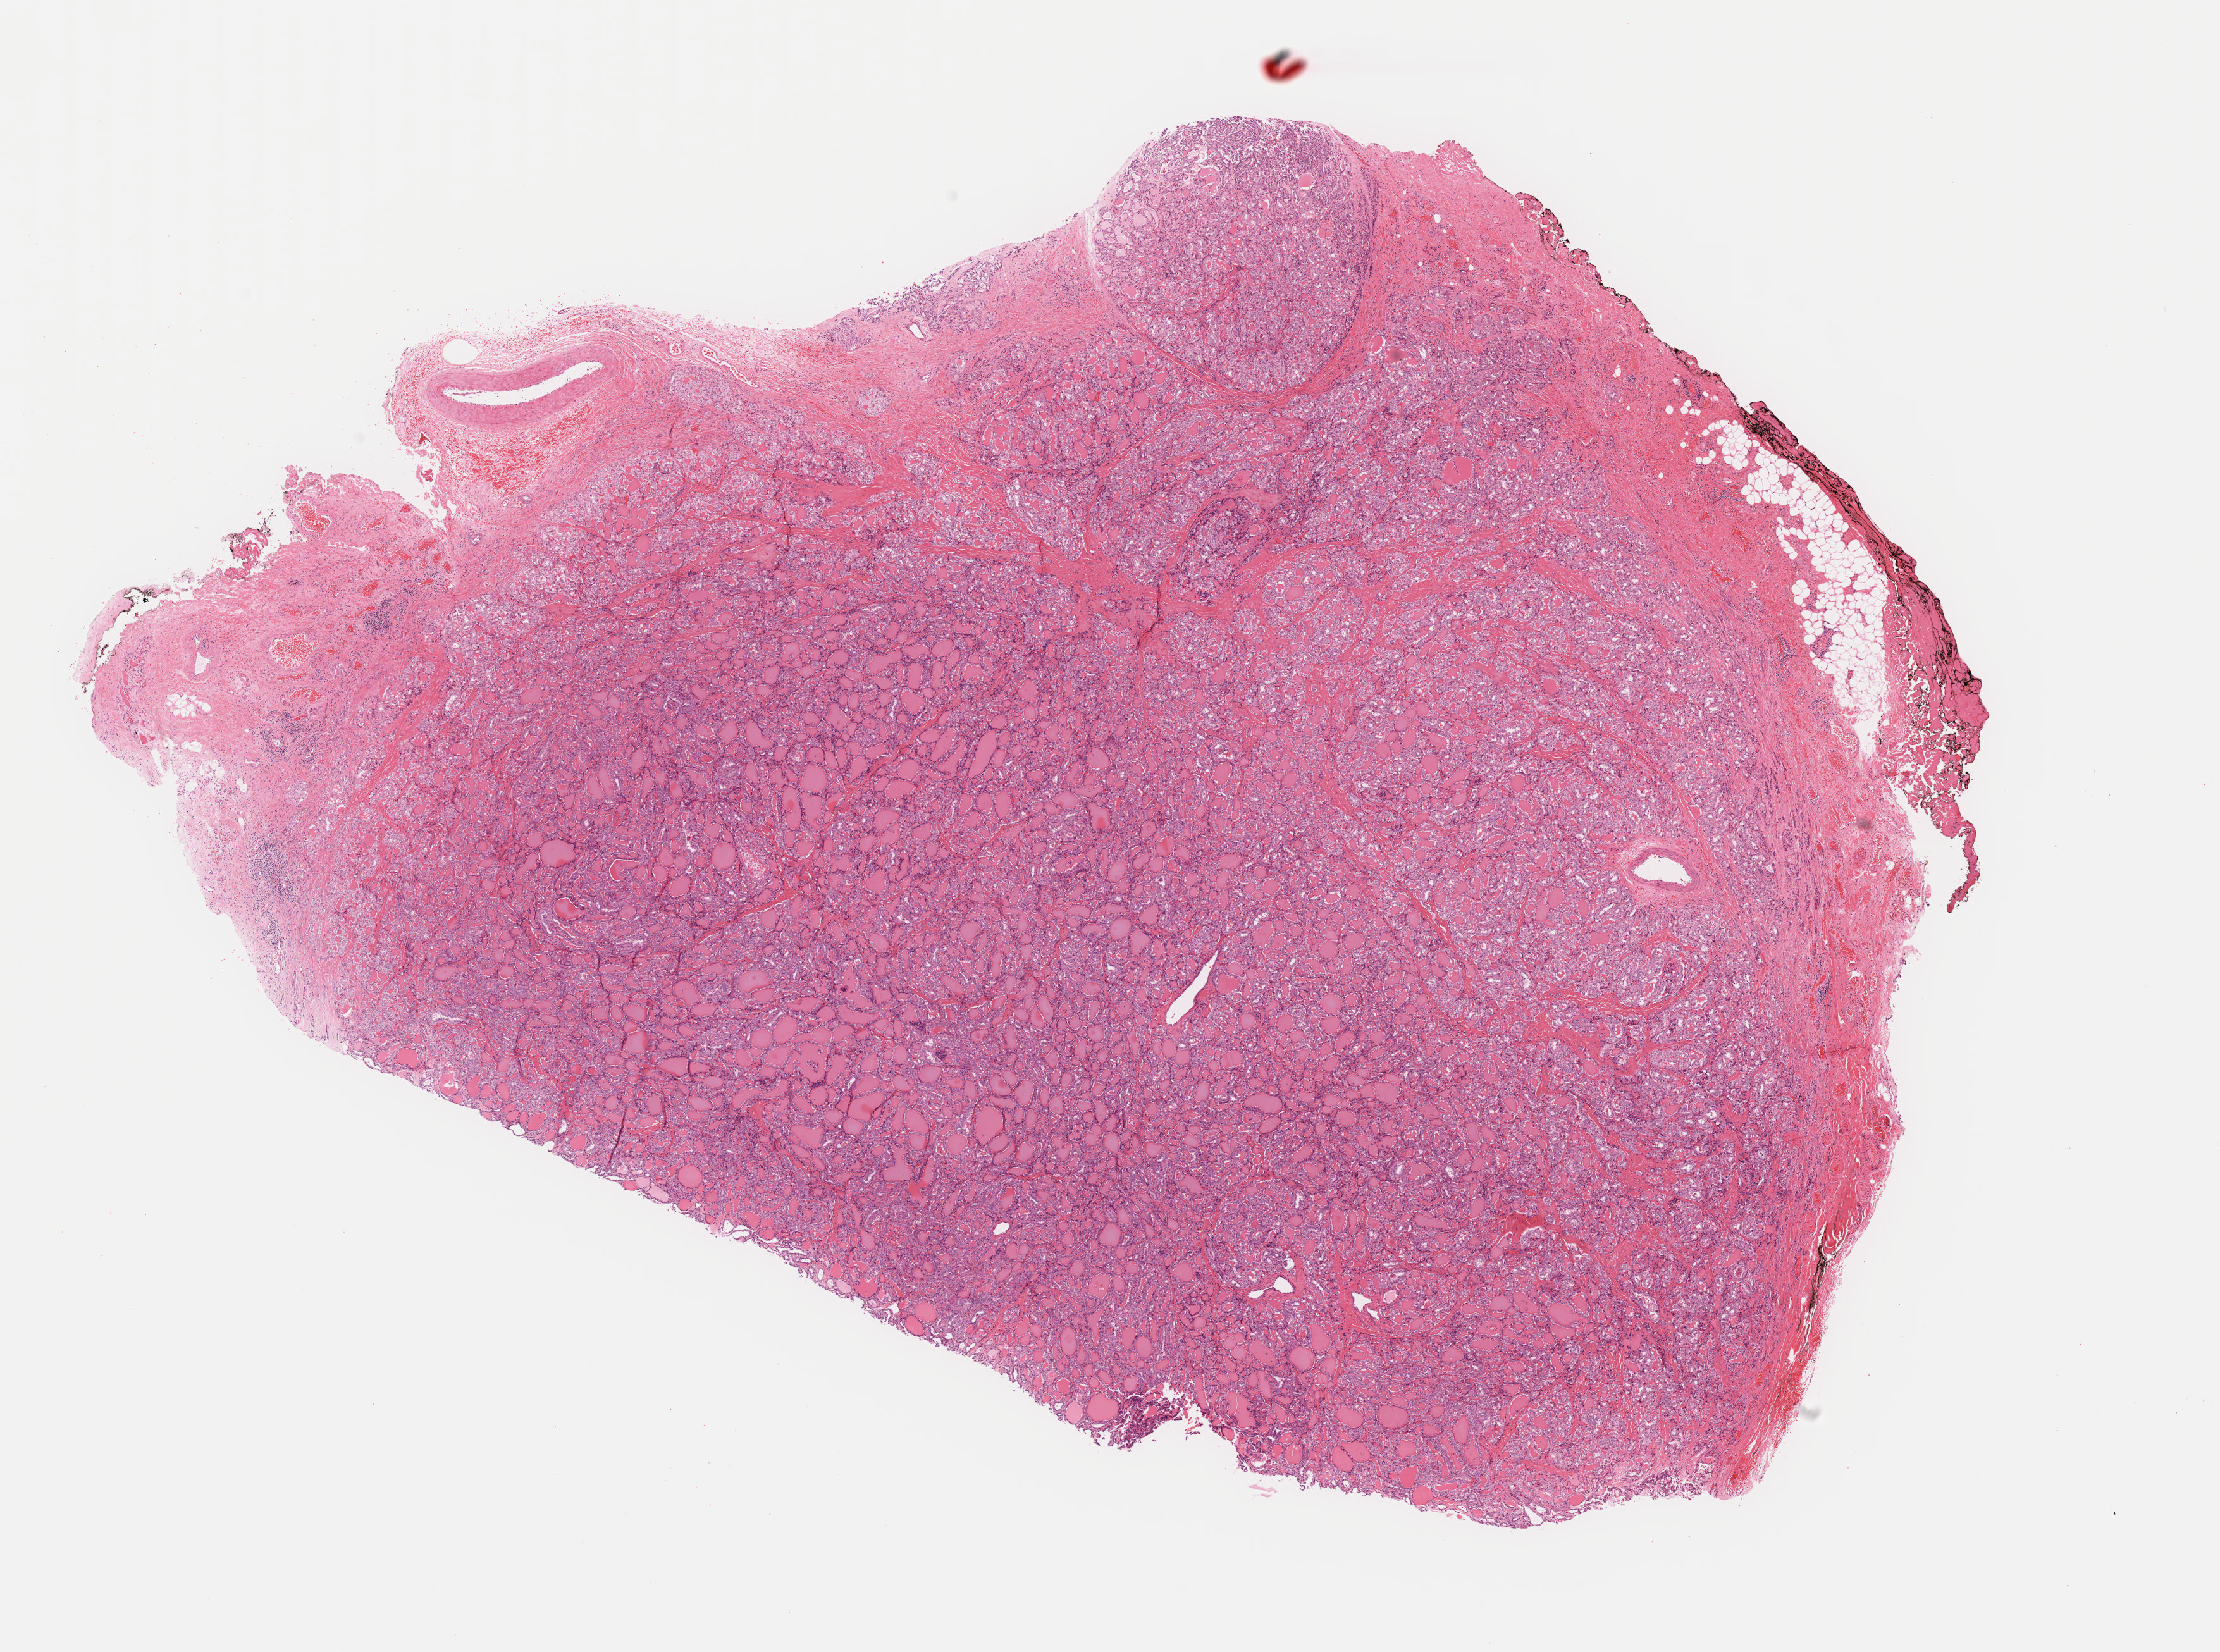
Whole-slide histology image, H&E-stained, shown as a low-resolution overview of the whole scanned area (about 13.9 x 10.3 mm, slide scanned at 40x). Formalin-fixed paraffin-embedded (FFPE) diagnostic section. Primary tumour sample from the thyroid. Female, age 23 years at initial diagnosis.
Lymph nodes positive (case pathology): 0 of 3 examined. Diagnosis: Papillary adenocarcinoma, NOS (thyroid gland). AJCC pathologic stage: I (7th edition).